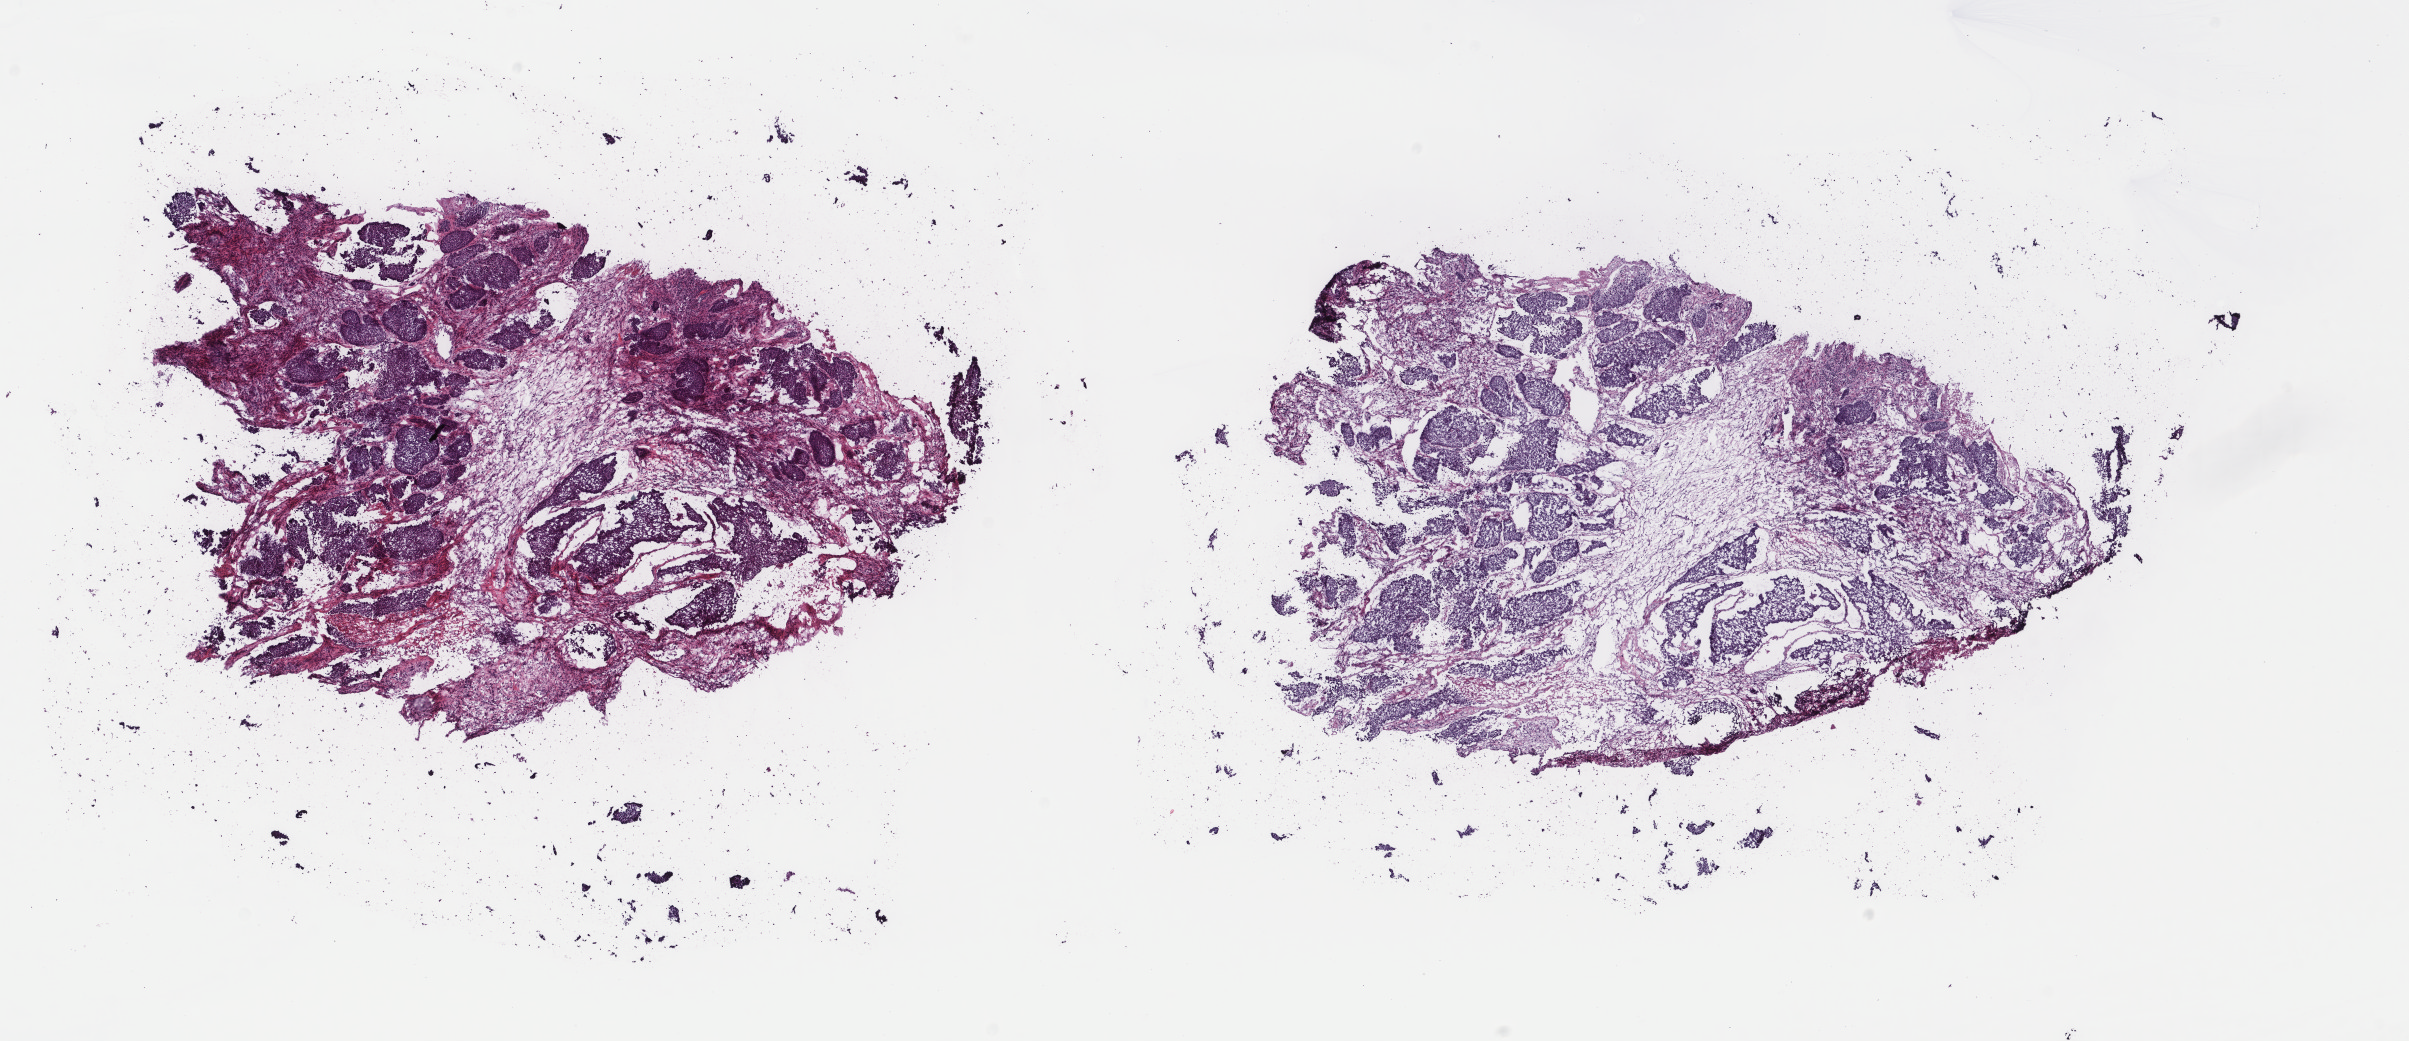
H&E-stained whole-slide image, shown as a low-resolution overview of the whole scanned area (about 19.1 x 8.3 mm); frozen section from the top of the tissue portion; primary tumour sample from the breast. Female, age 38 years at initial diagnosis. Slide review estimates, as recorded: tumour cells 70%, tumour nuclei 70%, normal cells 0%, stromal cells 30%, necrosis 0%. Infiltration values recorded for this section: lymphocyte infiltration 3%, monocyte infiltration 1%, neutrophil infiltration 1%.
Laterality: left. Pathologic diagnosis: Infiltrating duct mixed with other types of carcinoma. AJCC pathologic stage: IIA (5th edition). Lymph nodes positive (case pathology): 0 of 18 examined.